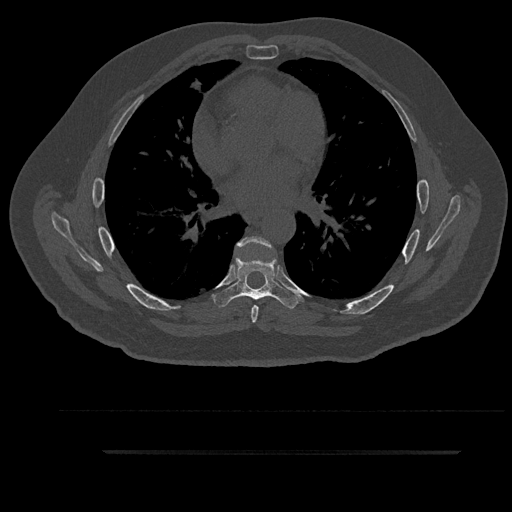
CT including the spine, one axial slice. Position 544 of 797 along the scan axis. Bone window (W 1800 / L 400 HU). 512 × 512 image matrix. Patient: male, 63 years. From the clinical record (not read from this slice): primary cancer: renal.
Annotated regions visible in this slice (semi-automatically segmented with operator editing):
- T6 vertebra: box from (x=236, y=236) to (x=271, y=323) px
- T7 vertebra: (x=213, y=256)–(x=299, y=309)